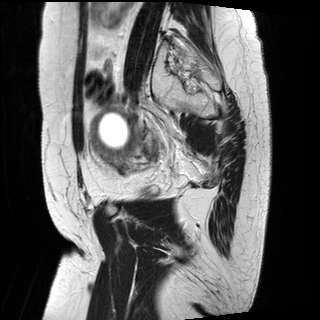
Pelvic MRI for cervical cancer, one sagittal slice. Slice 24 of 29 in the series (ordered by position). T2-weighted. 1.5 T. TE 89 ms, TR 2930 ms. 4 mm slice thickness. 320 × 320 image matrix, field of view 260 × 260 mm. Patient: female, 49 years.
Annotated regions visible in this slice (expert manual segmentation):
- uterus and cervix: bounding box [x1, y1, x2, y2] px = [90, 106, 137, 161]